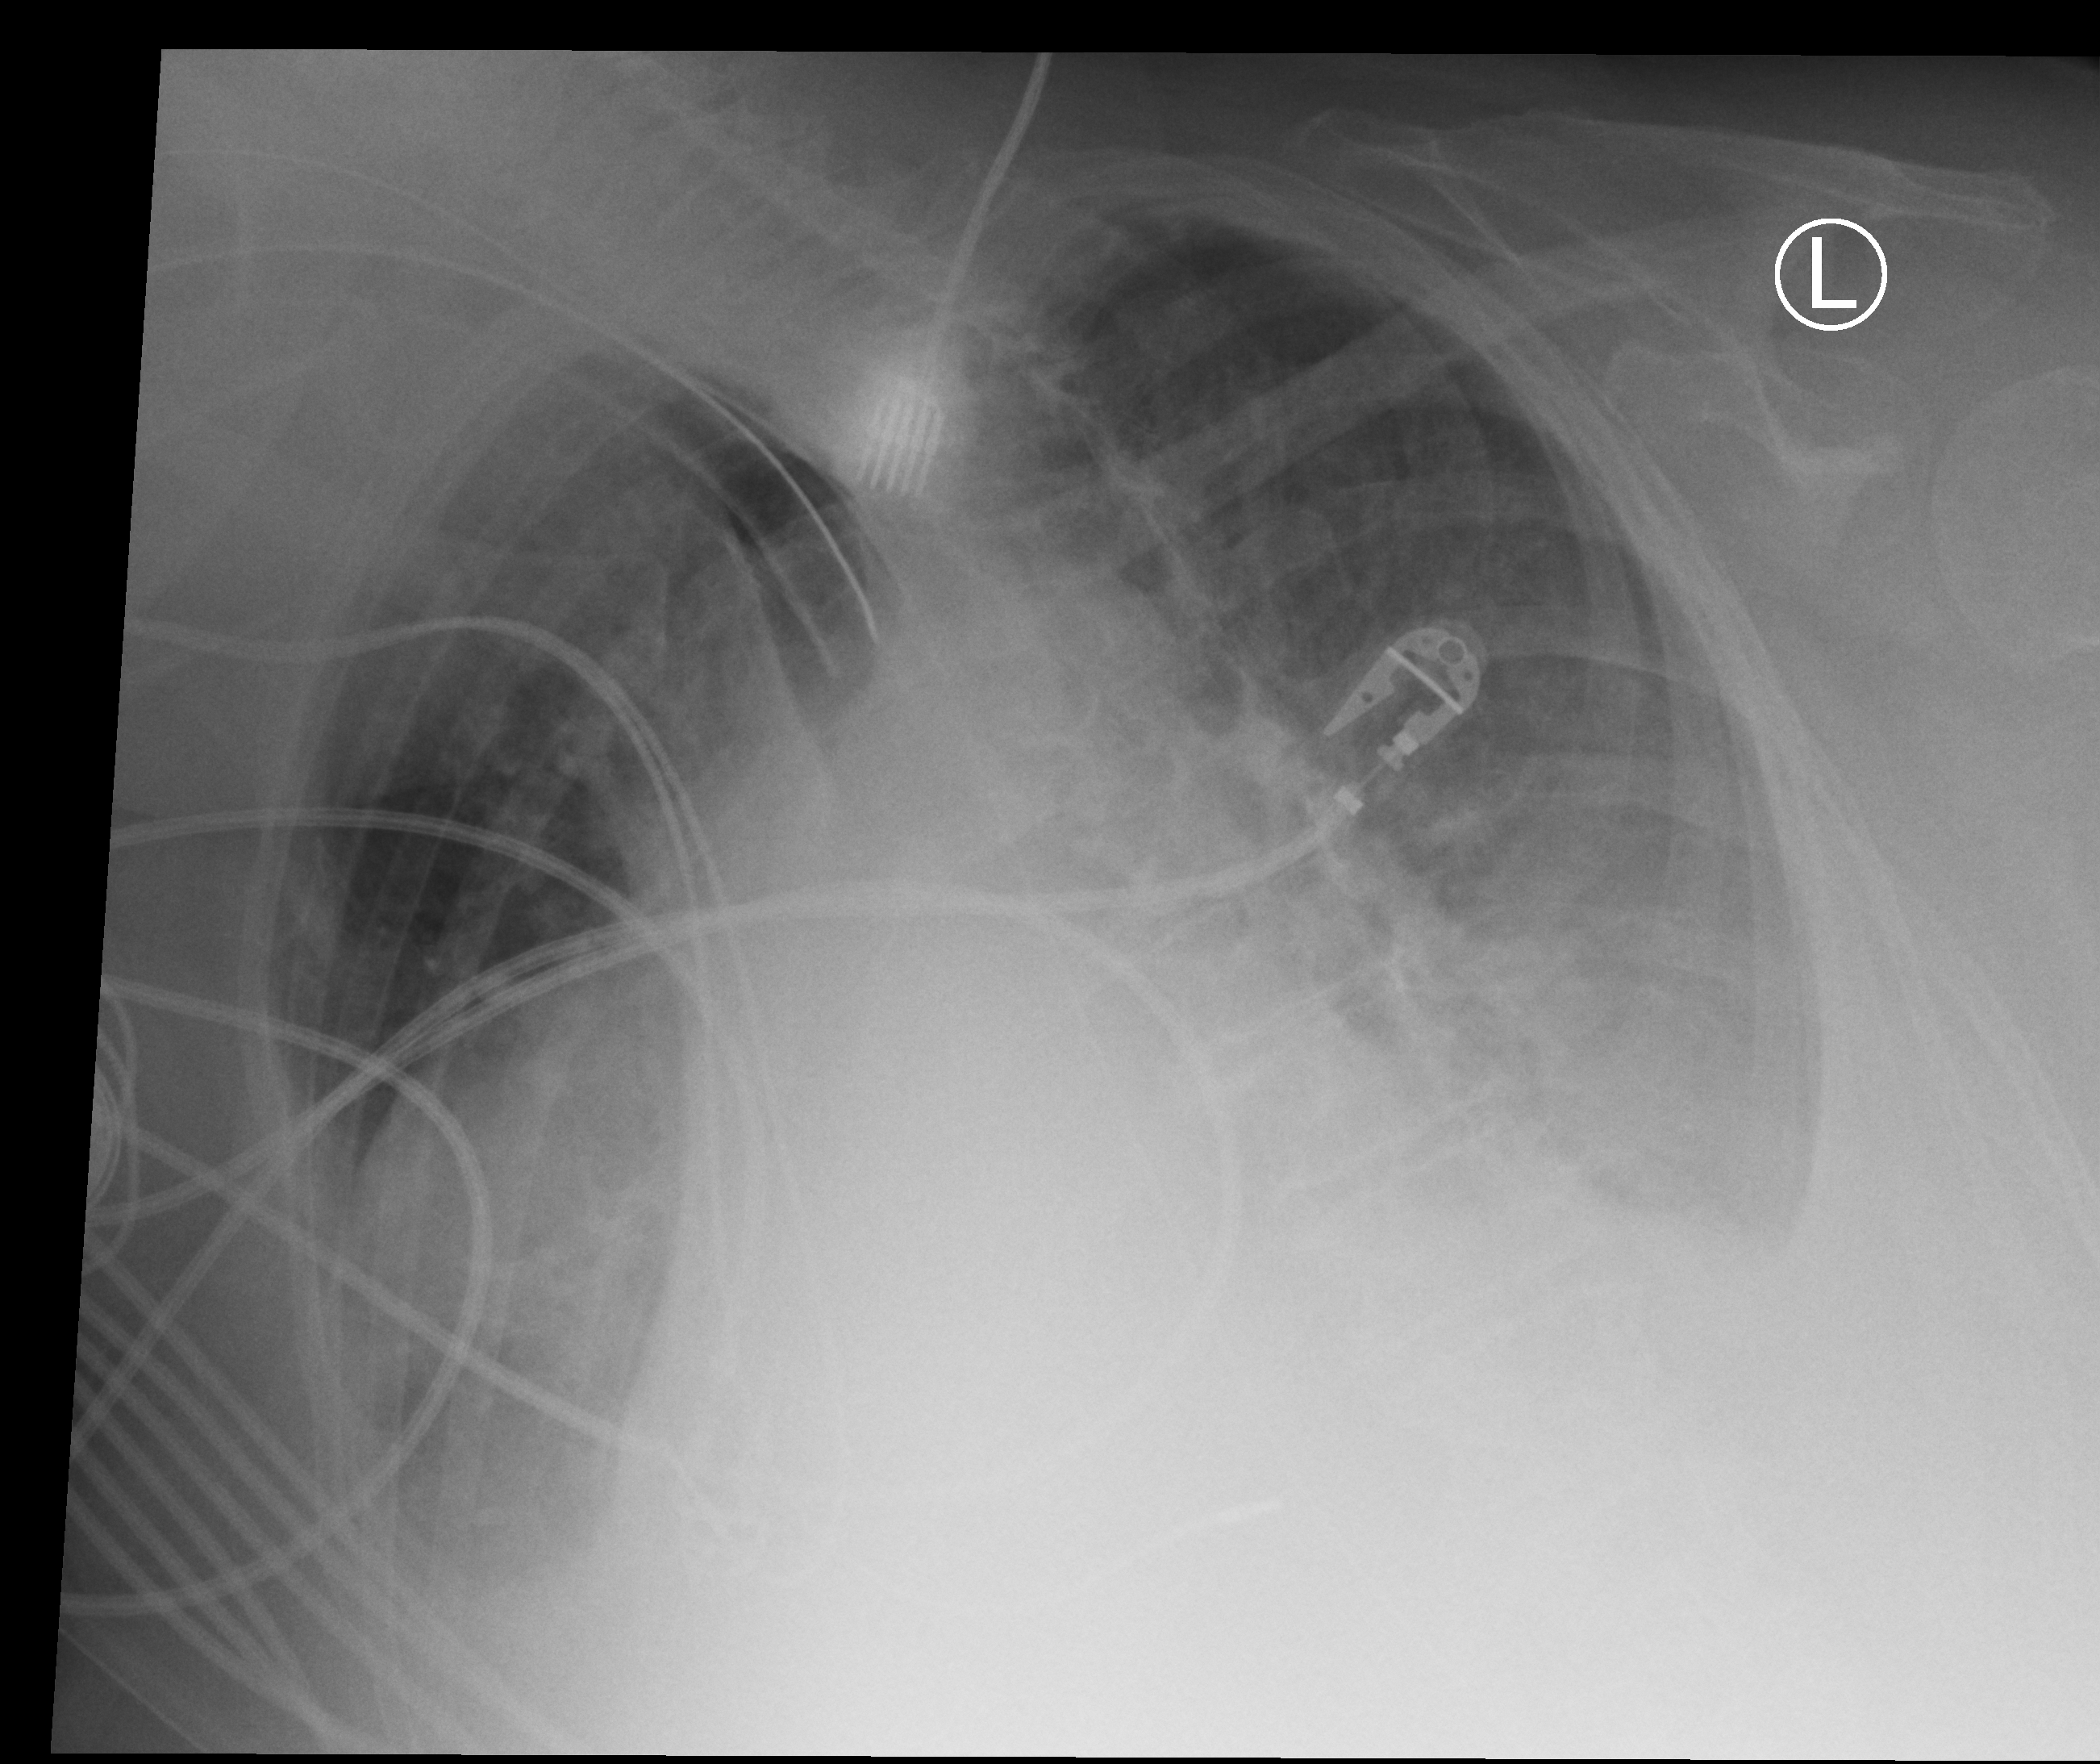
Portable chest radiograph; anteroposterior (AP) projection. Female patient hospitalised with COVID-19, age 75–90 years.
From the hospital-stay record, not from the radiograph (when in the stay this image was taken is not recorded):
- hypertension (admission record): yes
- smoking status (admission record): former
- COPD (admission record): yes